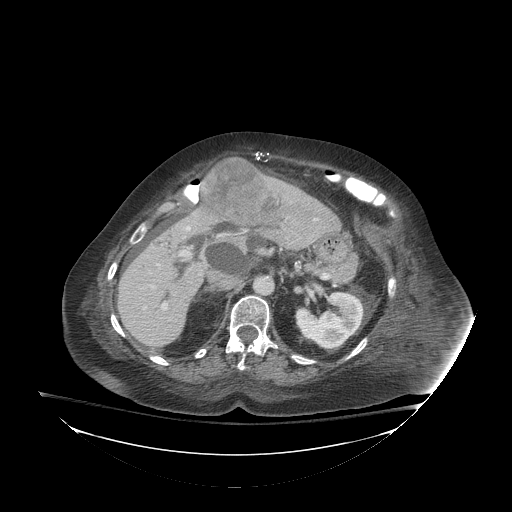
Contrast-enhanced abdominal CT (liver protocol), one axial slice; reconstruction kernel STANDARD; 140 kVp; soft-tissue window (W 400 / L 40 HU); 2.5 mm slice thickness; 512 × 512 image matrix, field of view 500 × 500 mm. Case-level facts recorded for this patient, not image findings: diagnosis: hepatocellular carcinoma (patient treated with transarterial chemoembolisation; whether this scan precedes or follows treatment is not stated here); TNM stage (as recorded): Stage-I; Child-Pugh class: B; tumour differentiation: well-moderately differentiated; tumour nodularity: uninodular.
Structures marked on this image (semi-automatic segmentation, software-assisted and operator-edited):
- liver parenchyma outside the tumour (the mass and vessels are separate outlines, so this box may not span the whole liver): bounding box <117,176,338,348> (left, top, right, bottom; pixels)
- mass: <201,157,279,225>
- liver vessels: <157,218,318,310>